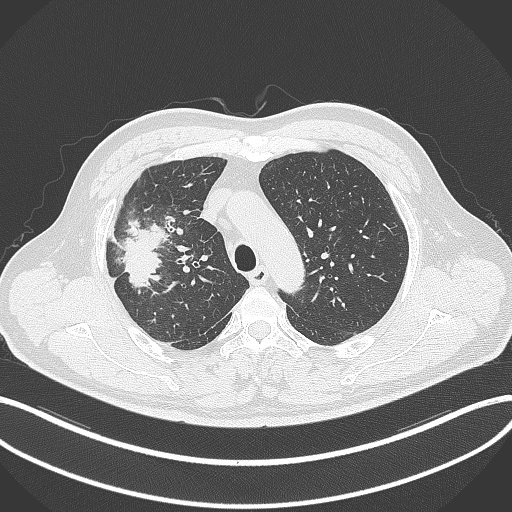
Chest CT, one axial slice; slice 254 of 348 in the series (ordered by position); reconstruction kernel B70f; 120 kVp; lung window (W 1500 / L -600 HU); 1 mm slice thickness; 512 × 512 image matrix, field of view 400 × 400 mm. Patient: male, 55 years. Case-level facts recorded for this patient, not image findings: clinical TNM (as recorded): T3 N2 M1.
Outlined on this slice (rectangle marked by the reading radiologist):
- lung tumour (recorded histology: adenocarcinoma): bounding box (x1, y1, x2, y2) in pixels: (118, 214, 169, 291)